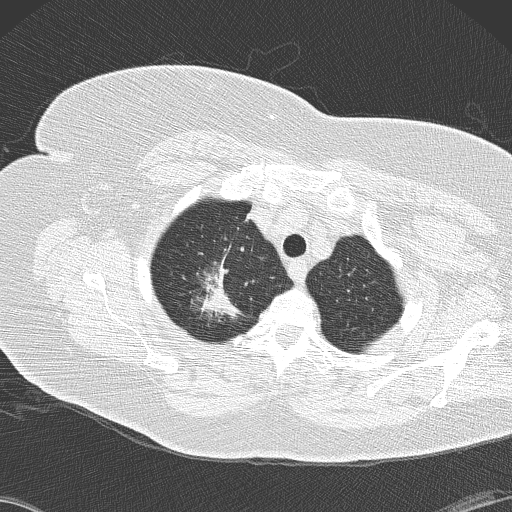
Low-dose screening chest CT, axial slice. Second annual screen. Lung window (W 1500 / L -600 HU). 2 mm slice thickness. 120 kVp. Slice 22 of 146 in the series. Female, age 72 years at enrolment. Former smoker at enrolment.
Expert-annotated lung lesion, box from (x=182, y=244) to (x=260, y=326) px. The screening reader recorded 4 non-calcified nodules or masses ≥4 mm on this exam (right lower lobe, right lower lobe, right lower lobe, right upper lobe); which of them this box marks is not recorded. Official screen result: positive, other.